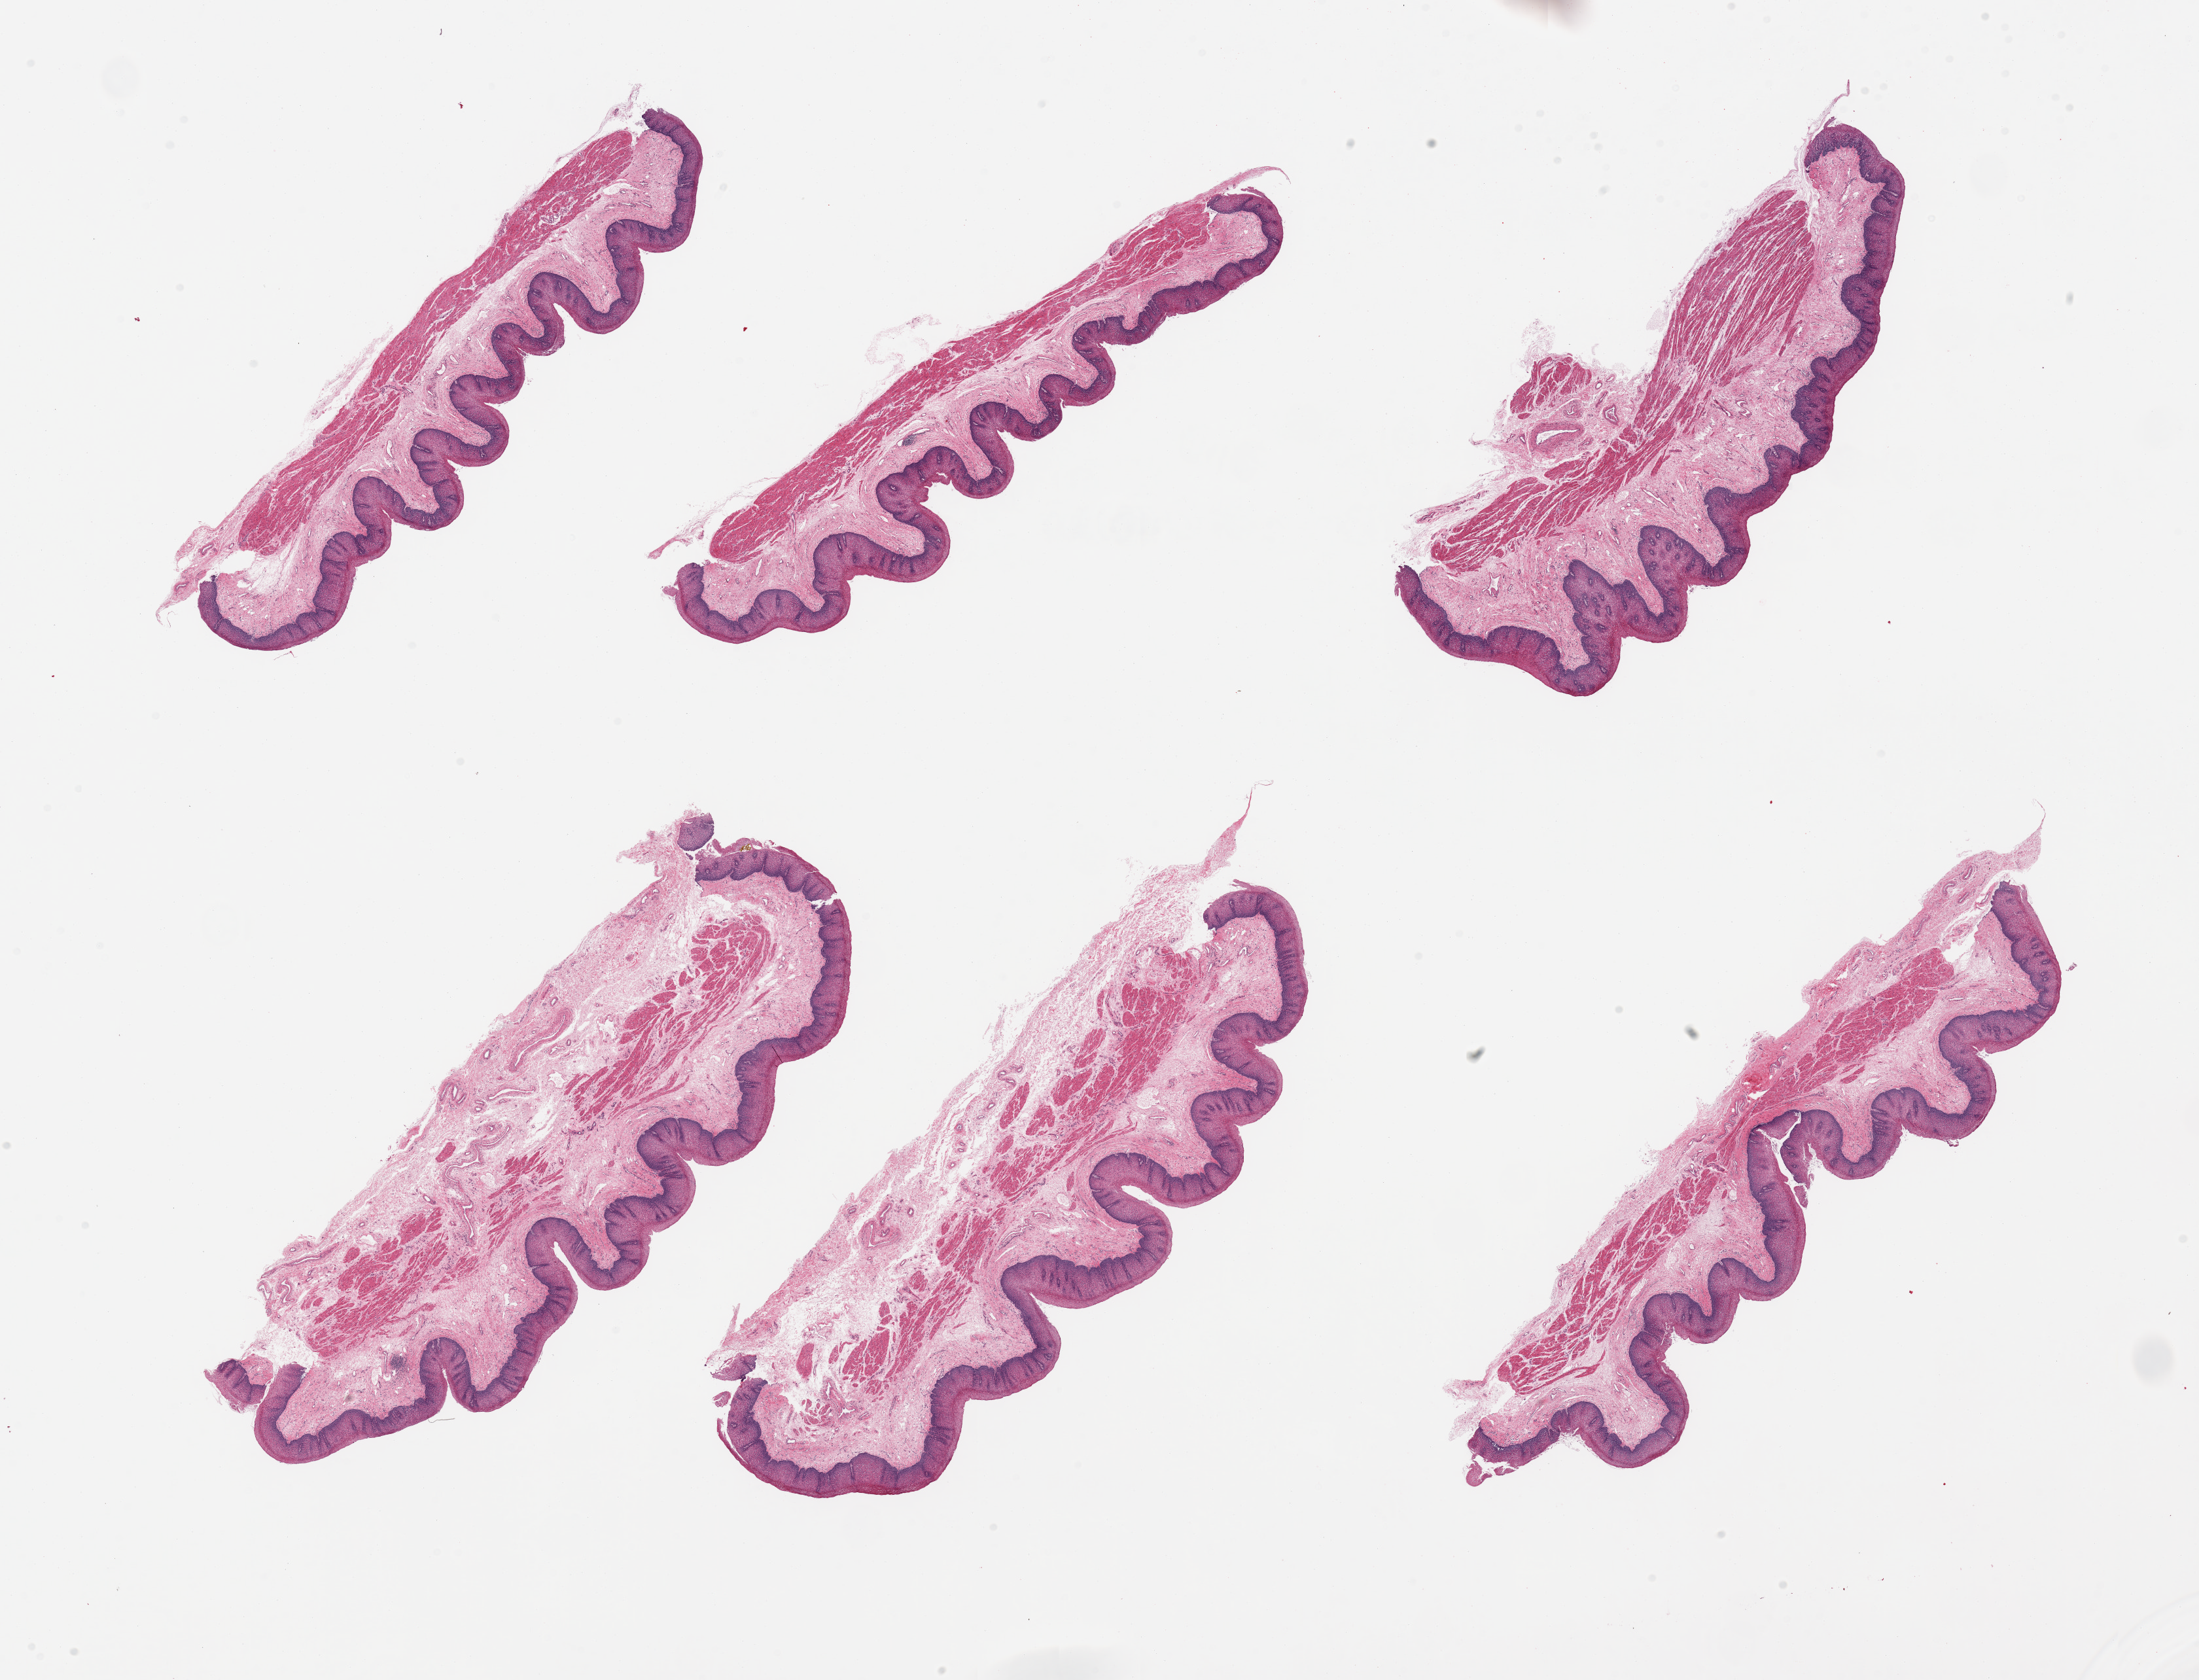
Whole-slide image, H&E stain, brightfield — shown as a low-resolution overview of the whole scanned area (about 26.6 x 20.3 mm). PAXgene-fixed paraffin-embedded (PFPE) section. Section of esophageal mucous membrane (target tissue). Donor tissue sample. Donor: male.
- review note (as recorded): 6 pieces; well preserved squamous epithelium up to 448 microns in thickness